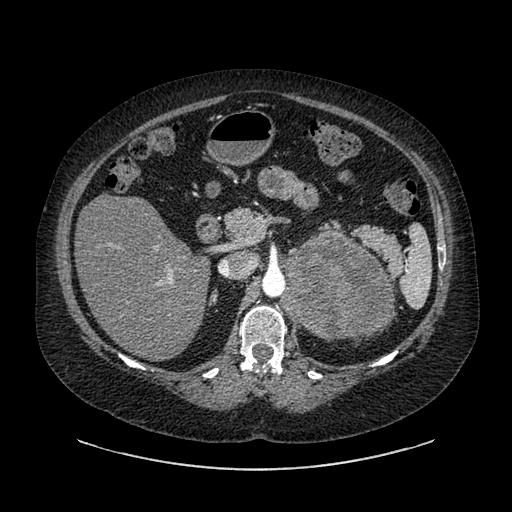
Contrast-enhanced abdominal CT, one axial slice; position 564 of 769 along the scan axis; reconstruction kernel SOFT; intravenous contrast given; soft-tissue window (W 400 / L 40 HU); 0.62 mm slice thickness; 512 × 512 image matrix, field of view 460 × 460 mm. Female patient, age 61 years. Case-level facts recorded for this patient, not image findings: diagnosis: adrenocortical carcinoma; tumour side: left adrenal; tumour size at pathology: 13 cm; Ki-67 index: 79 %; stage (as recorded): 2.
Structures marked on this image (semi-automatic segmentation, software-assisted and operator-edited):
- mass: bounding box <281,231,392,340> (left, top, right, bottom; pixels)